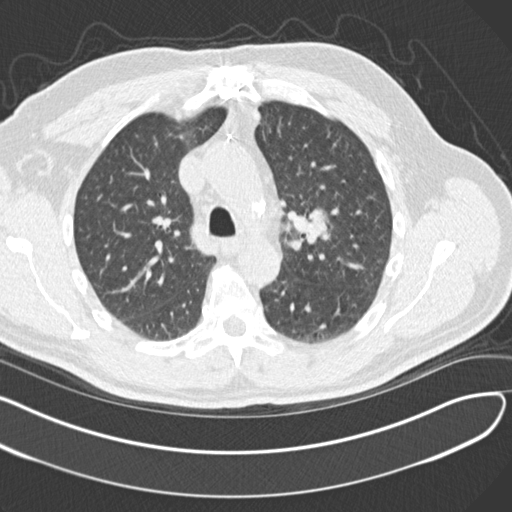
Axial slice from a low-dose chest CT screening exam, second screening round (one year after baseline), lung window (W 1500 / L -600 HU), 2 mm slice thickness, slice 47 of 164 in the series, 512 × 512 image matrix. Male participant, aged 65 years at enrolment. Former smoker at enrolment.
Expert reader's lesion annotation, bounding box <287,196,346,259> (left, top, right, bottom; pixels). The screening reader recorded 4 non-calcified nodules or masses ≥4 mm on this exam (left upper lobe, left upper lobe, left lower lobe, right middle lobe); which of them this box marks is not recorded. Official screen result: positive, other. Lung cancer was diagnosed 577 days after this screen (after the third annual screen): acinar cell carcinoma, left upper lobe, stage IA (AJCC 6th edition), 25 mm at pathology.